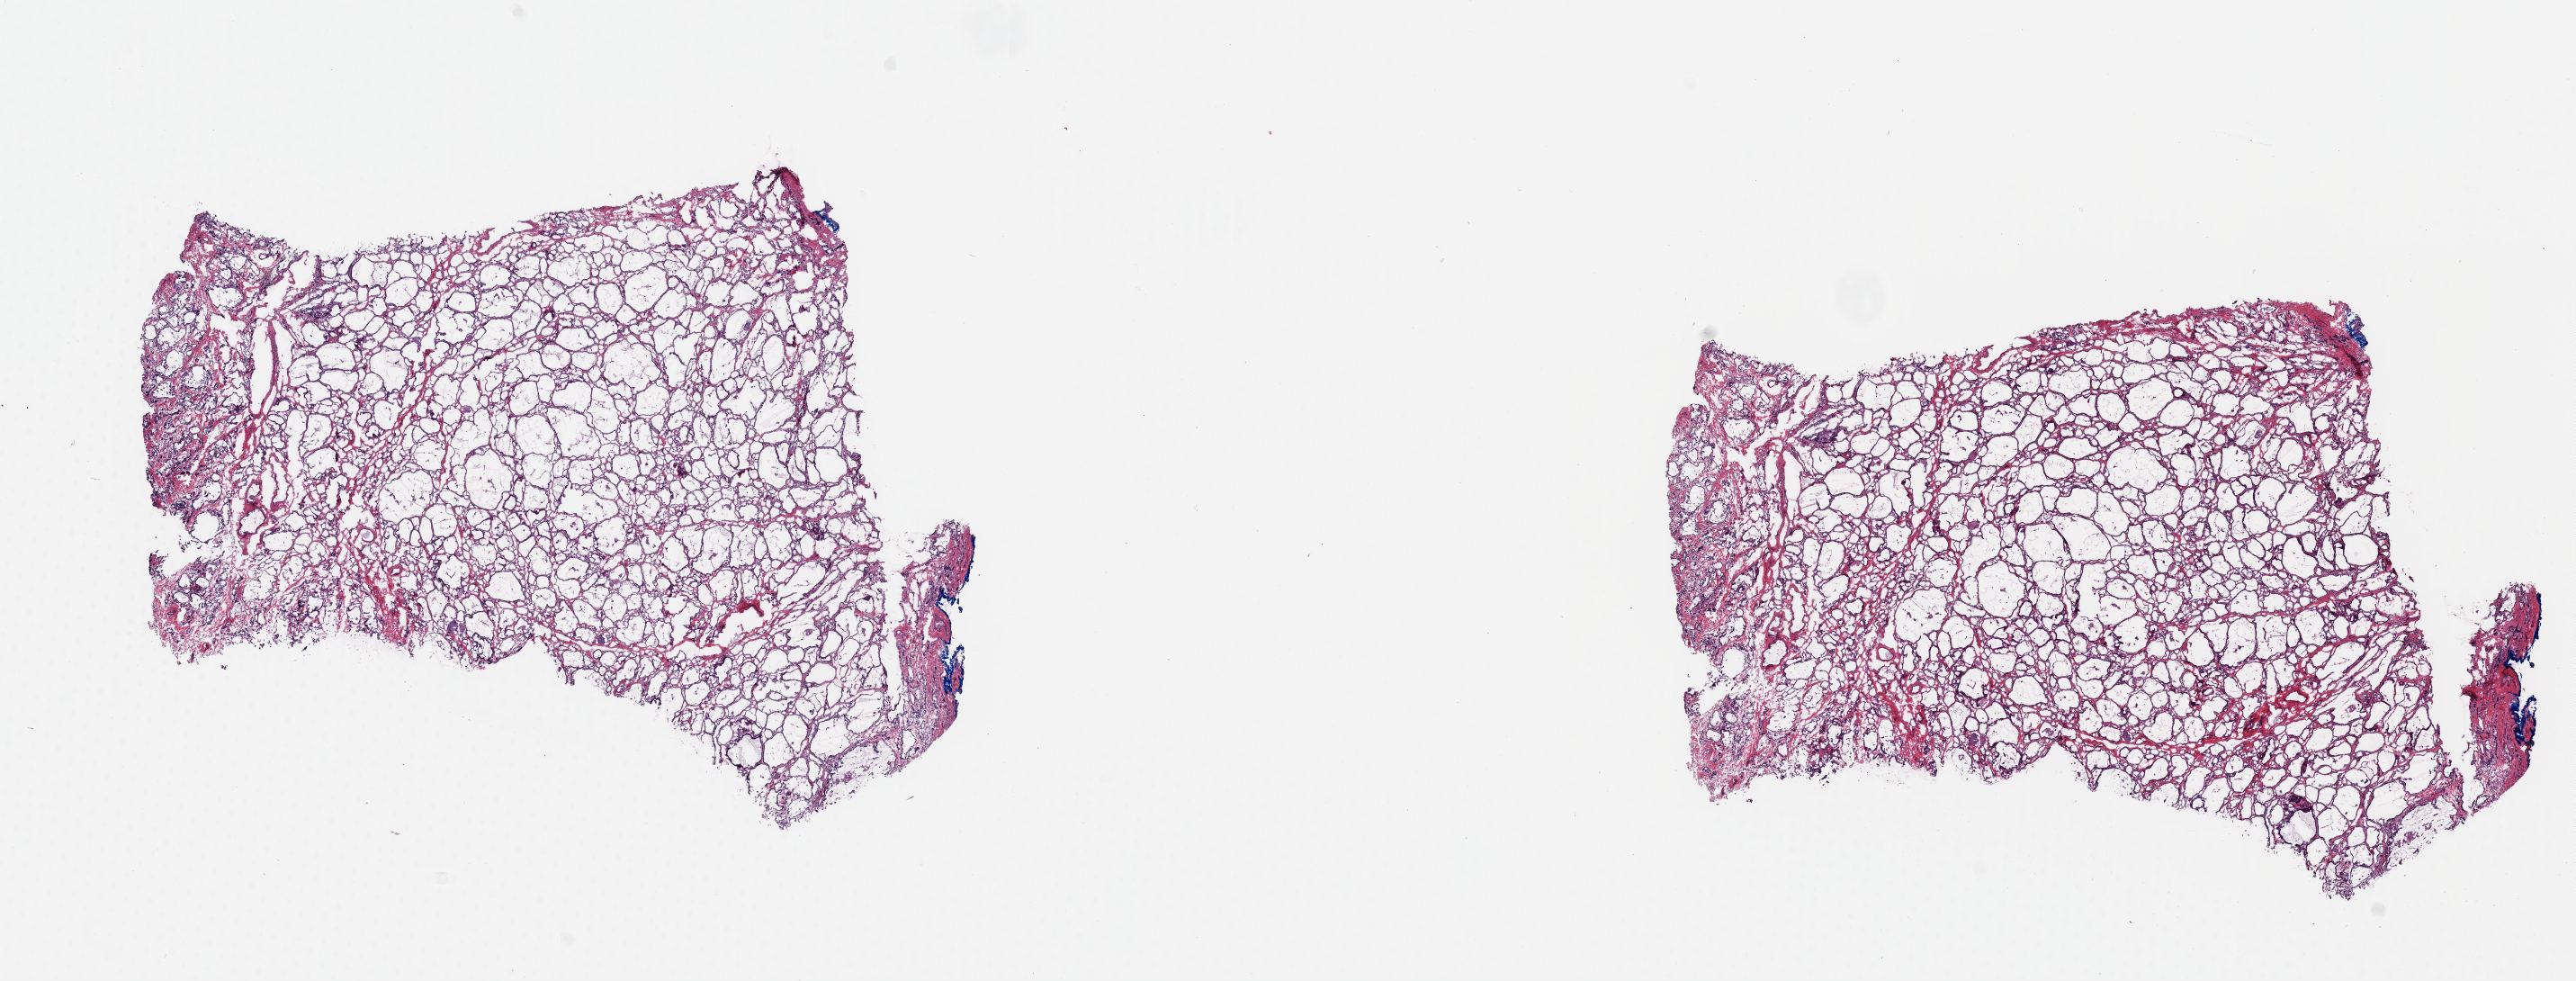
Digitized H&E tissue section (whole slide) — shown as a low-resolution overview of the whole scanned area (about 22.6 x 8.6 mm, slide scanned at 20x). Frozen section. Solid tissue normal (non-tumour tissue) sample from the thyroid. Female, age 46 years at initial diagnosis. Composition of this section per pathologist review: tumour cells 0%, tumour nuclei 0%, normal cells 100%, stromal cells 0%, necrosis 0%. Inflammatory infiltration, as recorded: lymphocyte infiltration 3%, monocyte infiltration 4%, neutrophil infiltration 0%.
* this section: solid tissue normal sample (biorepository sample class)
* patient diagnosis: Papillary adenocarcinoma, NOS (thyroid gland)